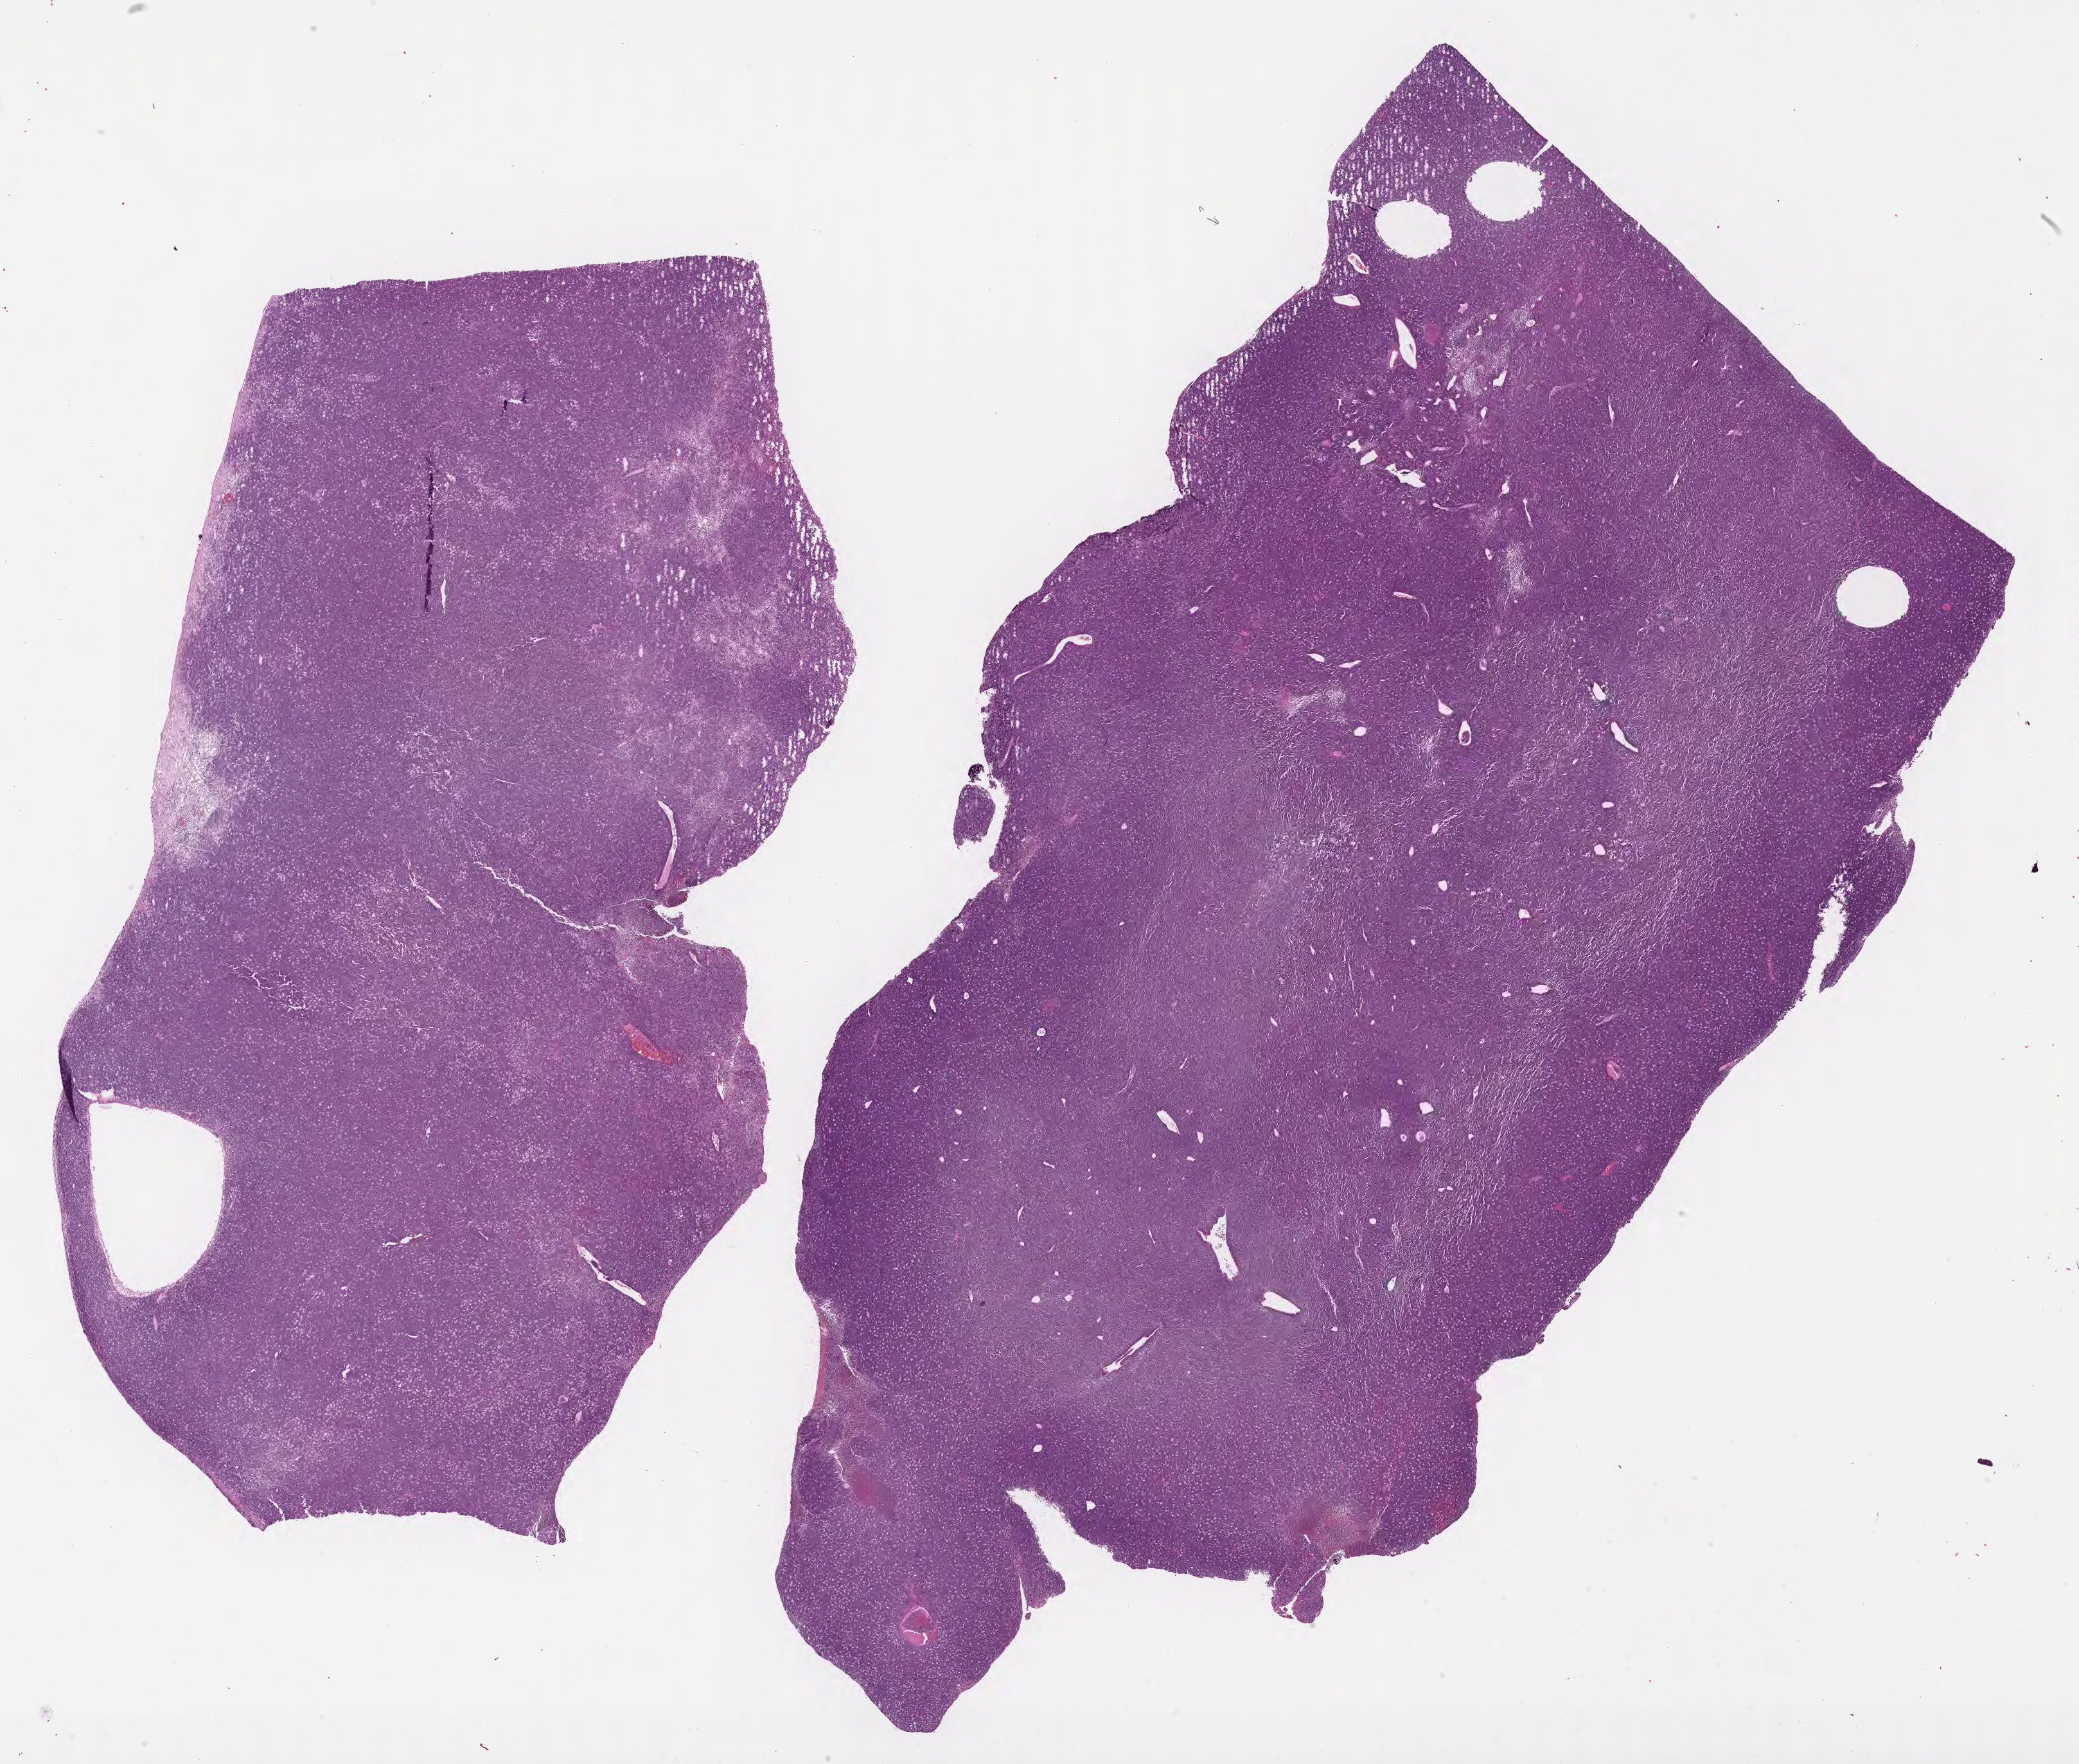
Digitized haematoxylin and eosin-stained section — shown as a low-resolution overview of the whole scanned area (about 26.2 x 22.2 mm); FFPE section; specimen: primary tumor. Patient: female, age 34 years. Pathologist review of this section (percent, as recorded): tumor cells 90%, tumor nuclei 95%, stromal cells 5%, necrosis 5%, normal cells 0%. Inflammatory infiltration, as recorded: lymphocyte infiltration 30%, monocyte infiltration 30%, neutrophil infiltration 5%.
Ann Arbor stage (patient): Stage IV. Diagnosis: Burkitt lymphoma, NOS.